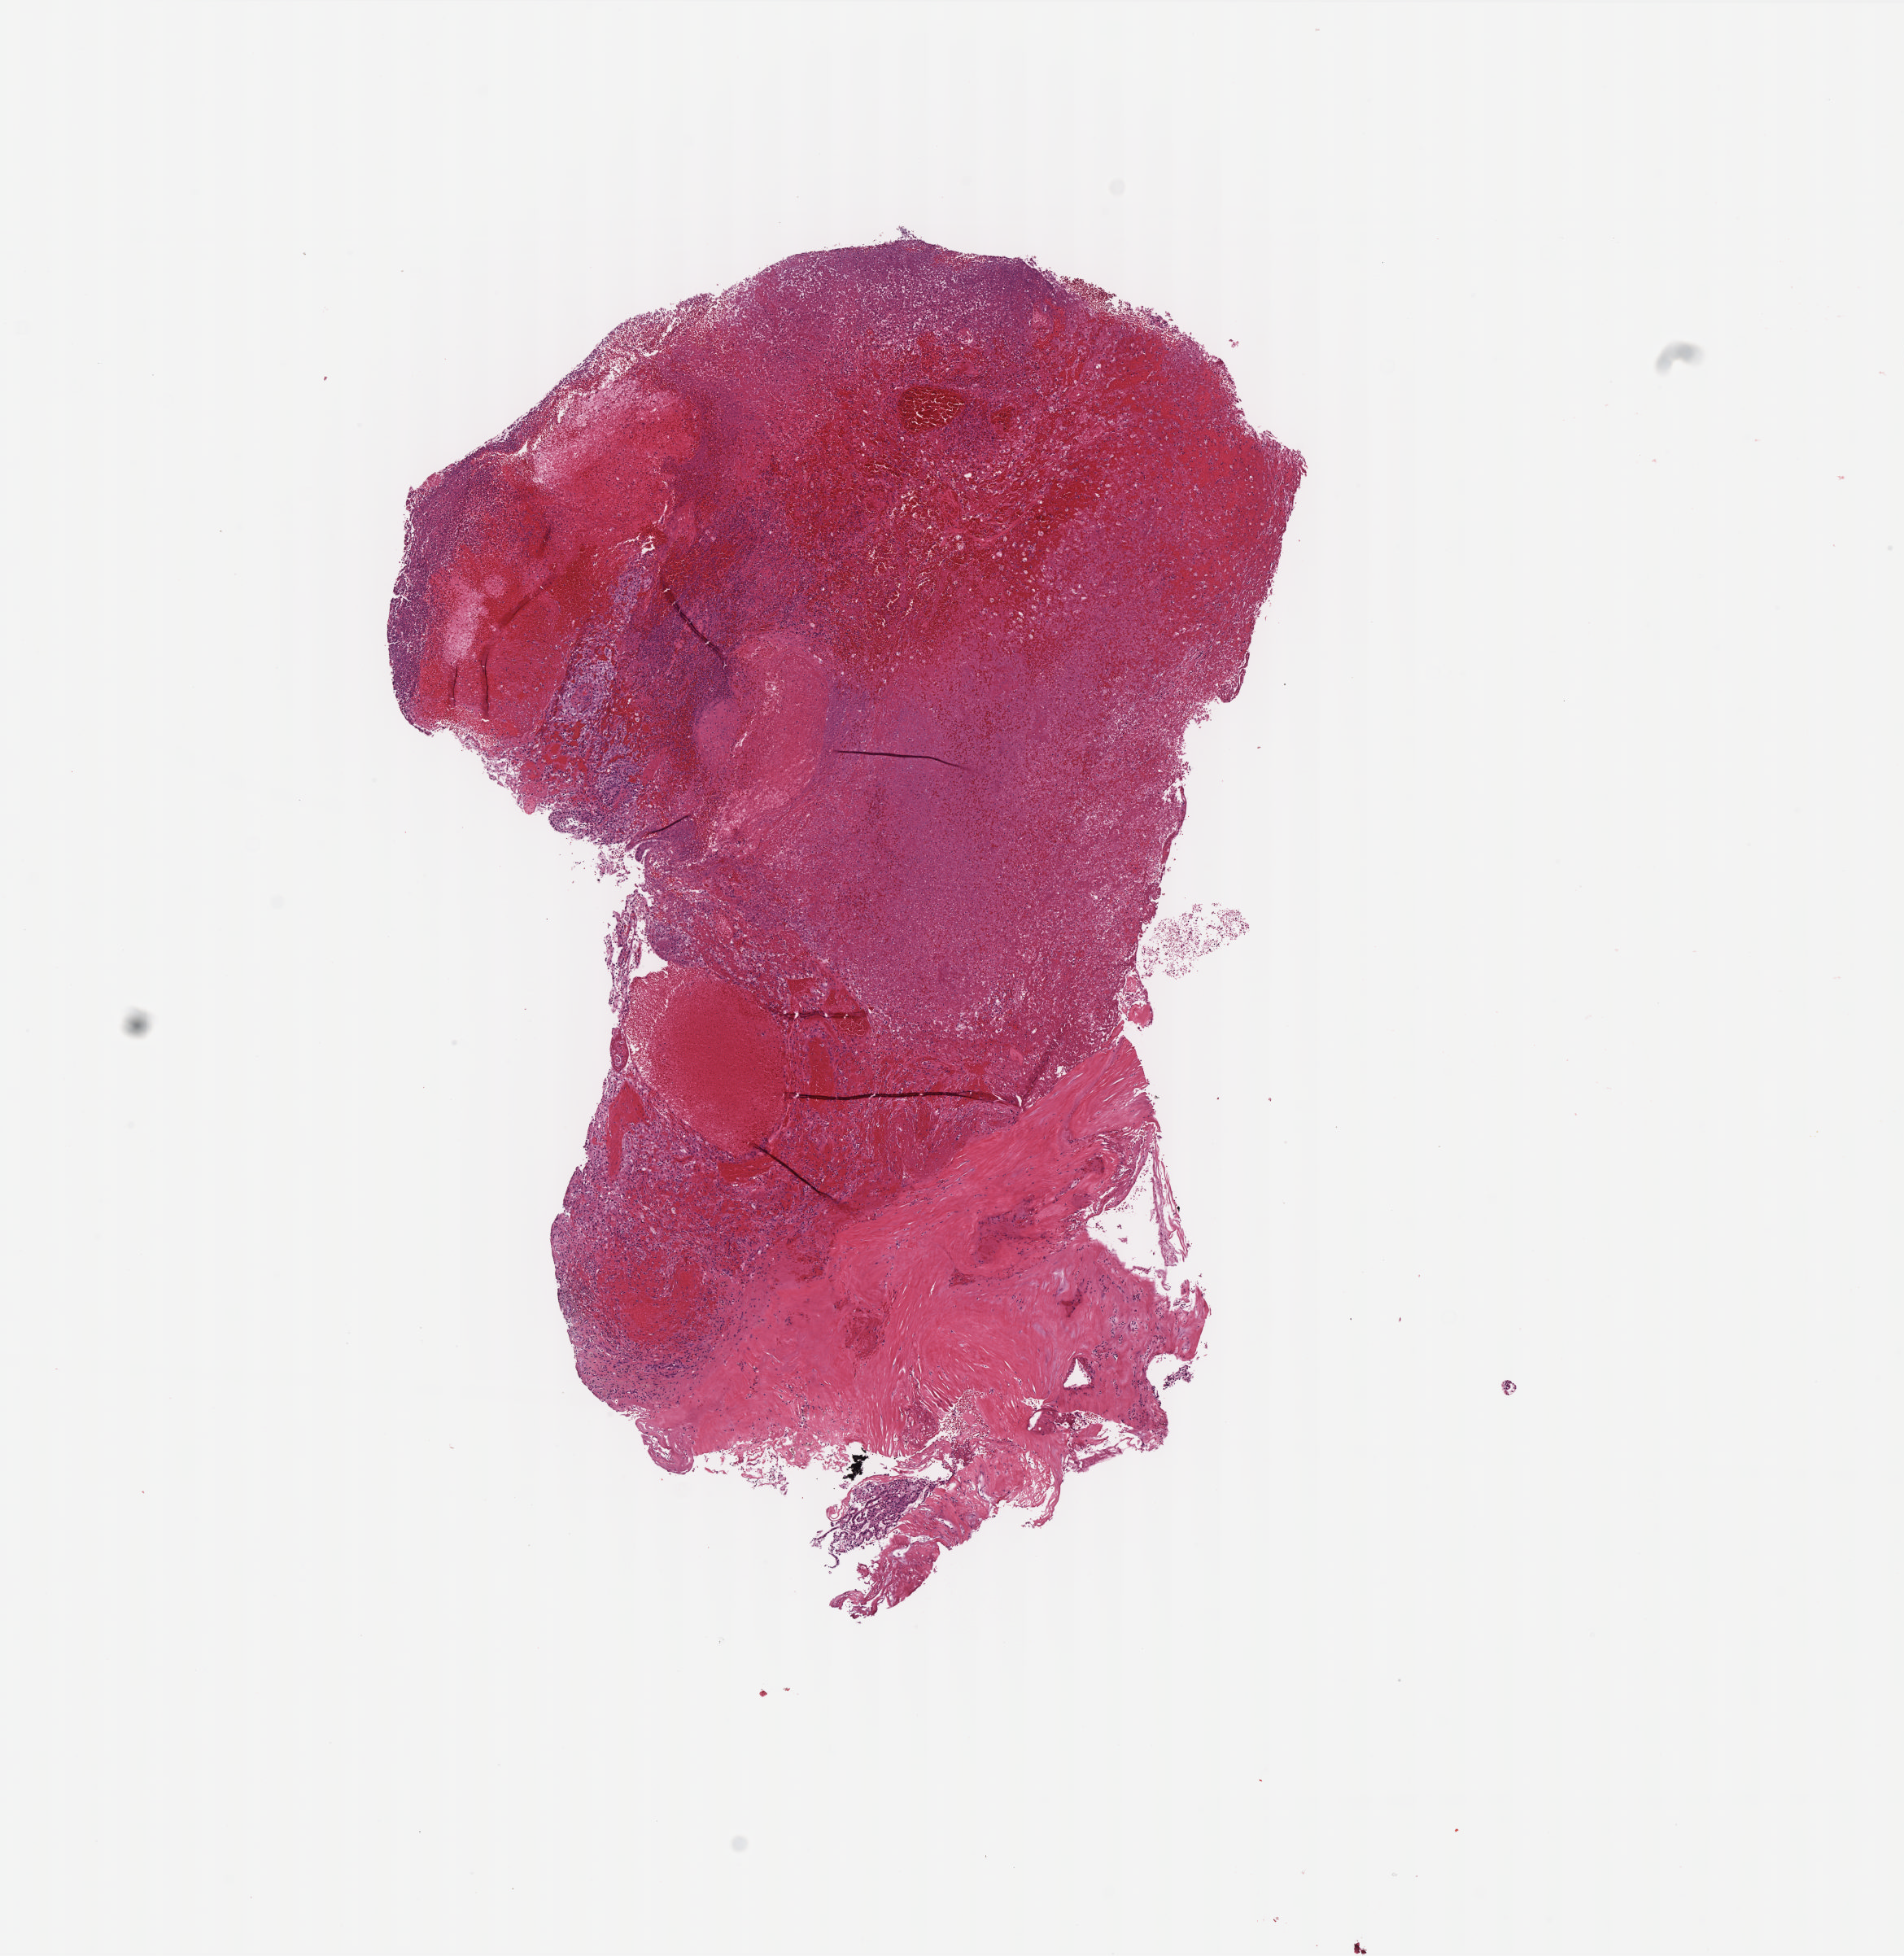
Whole-slide histology image, H&E-stained, a low-resolution overview of the entire scanned area, about 9.4 x 9.6 mm (acquisition: 40x scan). Formalin-fixed paraffin-embedded (FFPE) diagnostic section. Sample: primary tumour, kidney. Patient: female, age at initial diagnosis 48 years.
• diagnosis: Papillary adenocarcinoma, NOS
• AJCC pathologic stage: I (7th edition)
• laterality: right